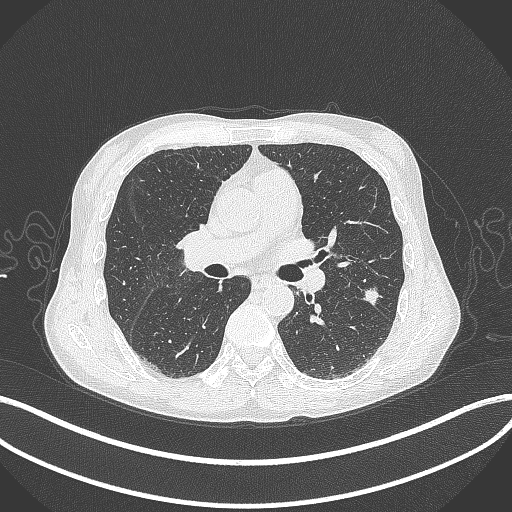
Chest CT, one axial slice; slice 202 of 429 in the series (ordered by position); reconstruction kernel B70f; lung window (W 1500 / L -600 HU); 1 mm slice thickness; 512 × 512 image matrix, field of view 400 × 400 mm. Patient: male, 58 years. From the clinical record (not read from this slice): clinical TNM (as recorded): T1c N0 M0; histopathological grade: G2.
Outlined on this slice (bounding box drawn by a radiologist):
- lung tumour (recorded histology: adenocarcinoma): bounding box [x1, y1, x2, y2] px = [362, 285, 383, 303]